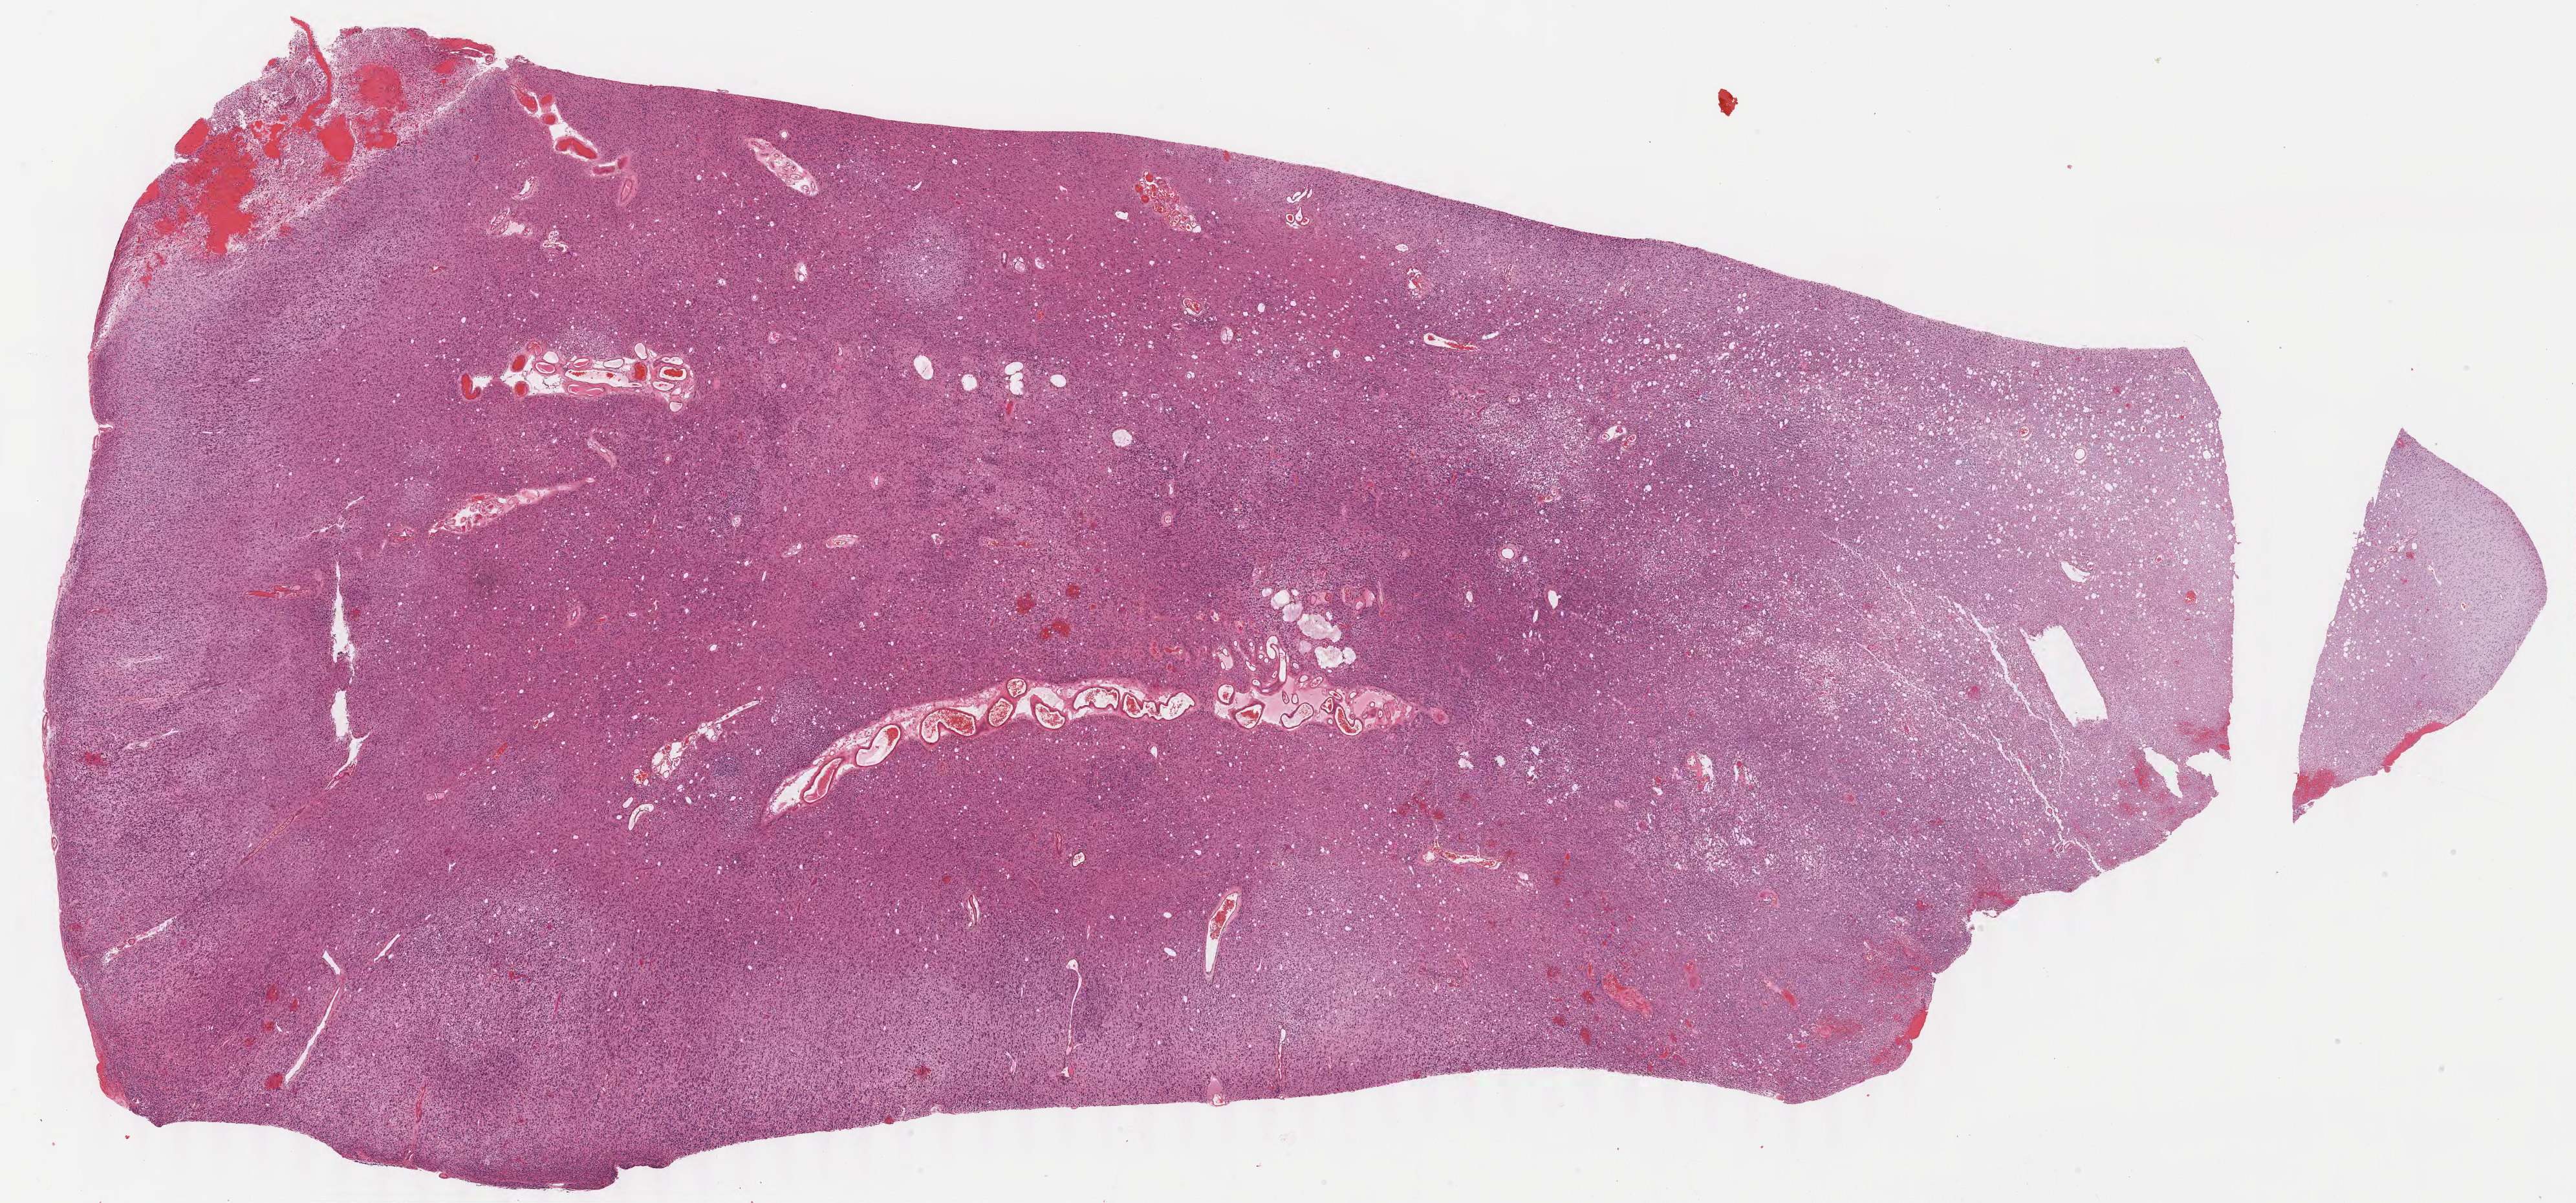
Whole-slide histology image, H&E-stained, whole scanned area (about 31.5 x 14.7 mm, from a 40x scan) shown as a low-resolution overview, formalin-fixed paraffin-embedded (FFPE) diagnostic section, brain, primary tumour sample. Female patient; age at initial diagnosis 67 years. Histologic grade: G2 (moderately differentiated).
Pathologic diagnosis: Oligodendroglioma, NOS.